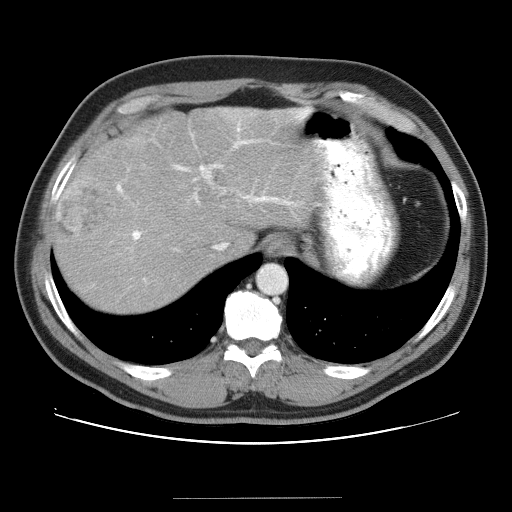
Contrast-enhanced abdominal CT (liver protocol), one axial slice. Position 29 of 40 along the scan axis. Soft-tissue window (W 400 / L 40 HU). 5 mm slice thickness. 512 × 512 image matrix, field of view 380 × 380 mm. From the clinical record (not read from this slice): diagnosis: hepatocellular carcinoma (patient treated with transarterial chemoembolisation; whether this scan precedes or follows treatment is not stated here); TNM stage (as recorded): Stage-IVA; Child-Pugh class: B.
Outlined on this slice (semi-automatic segmentation, software-assisted and operator-edited):
- abdominal aorta: bounding box <257,265,286,294> (left, top, right, bottom; pixels)
- liver parenchyma outside the tumour (the mass and vessels are separate outlines, so this box may not span the whole liver): <54,108,324,312>
- mass: <56,176,118,240>
- liver vessels: <116,109,310,250>